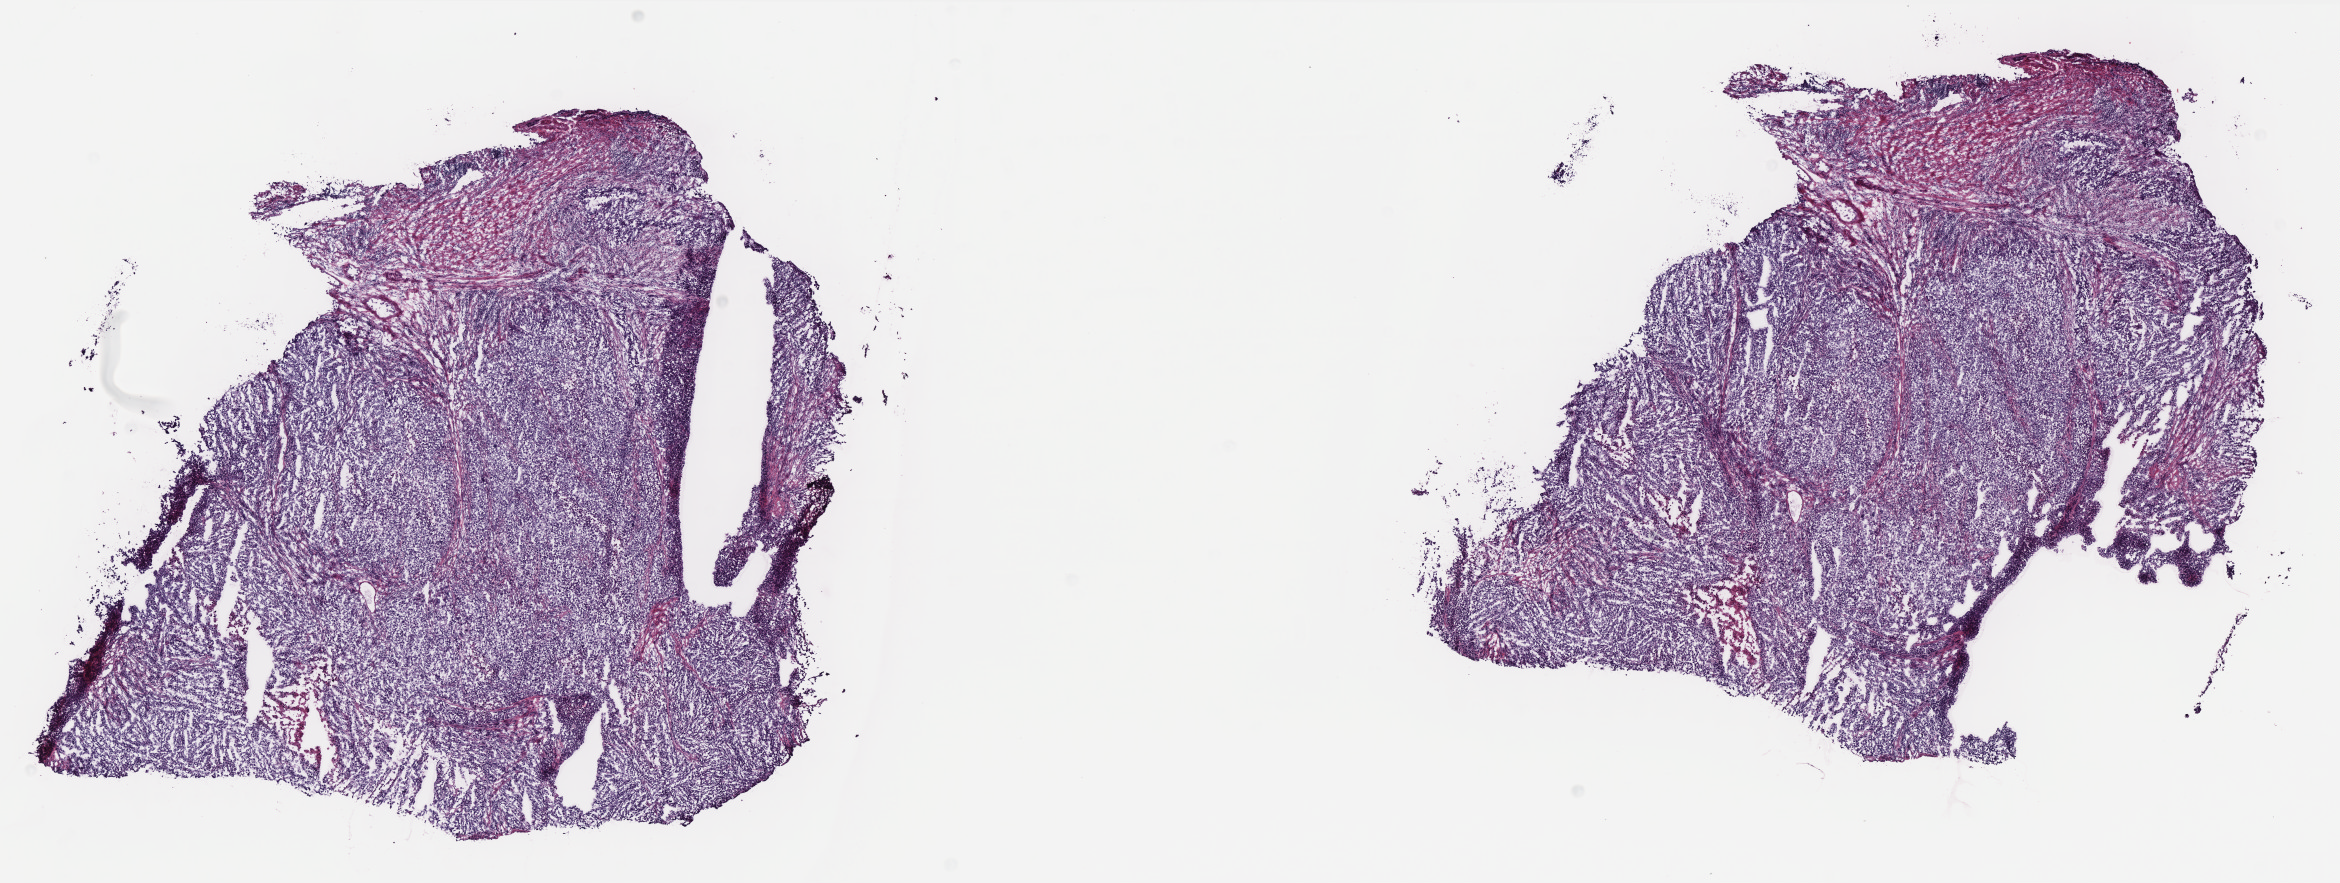
Digitized H&E-stained tissue section (whole slide) — low-resolution overview of the scanned area, about 18.8 x 7.1 mm, frozen section from the top of the tissue portion, primary tumour sample from the uterus. Female patient; age at initial diagnosis 57 years. Histologic grade: G3 (poorly differentiated). Slide review estimates, as recorded: tumour cells 85%, tumour nuclei 90%, normal cells 10%, stromal cells 0%, necrosis 5%. Inflammatory infiltration, as recorded: lymphocyte infiltration 20%, monocyte infiltration 0%, neutrophil infiltration 5%.
* histologic diagnosis: Serous cystadenocarcinoma, NOS (endometrium)
* FIGO stage: IIIB